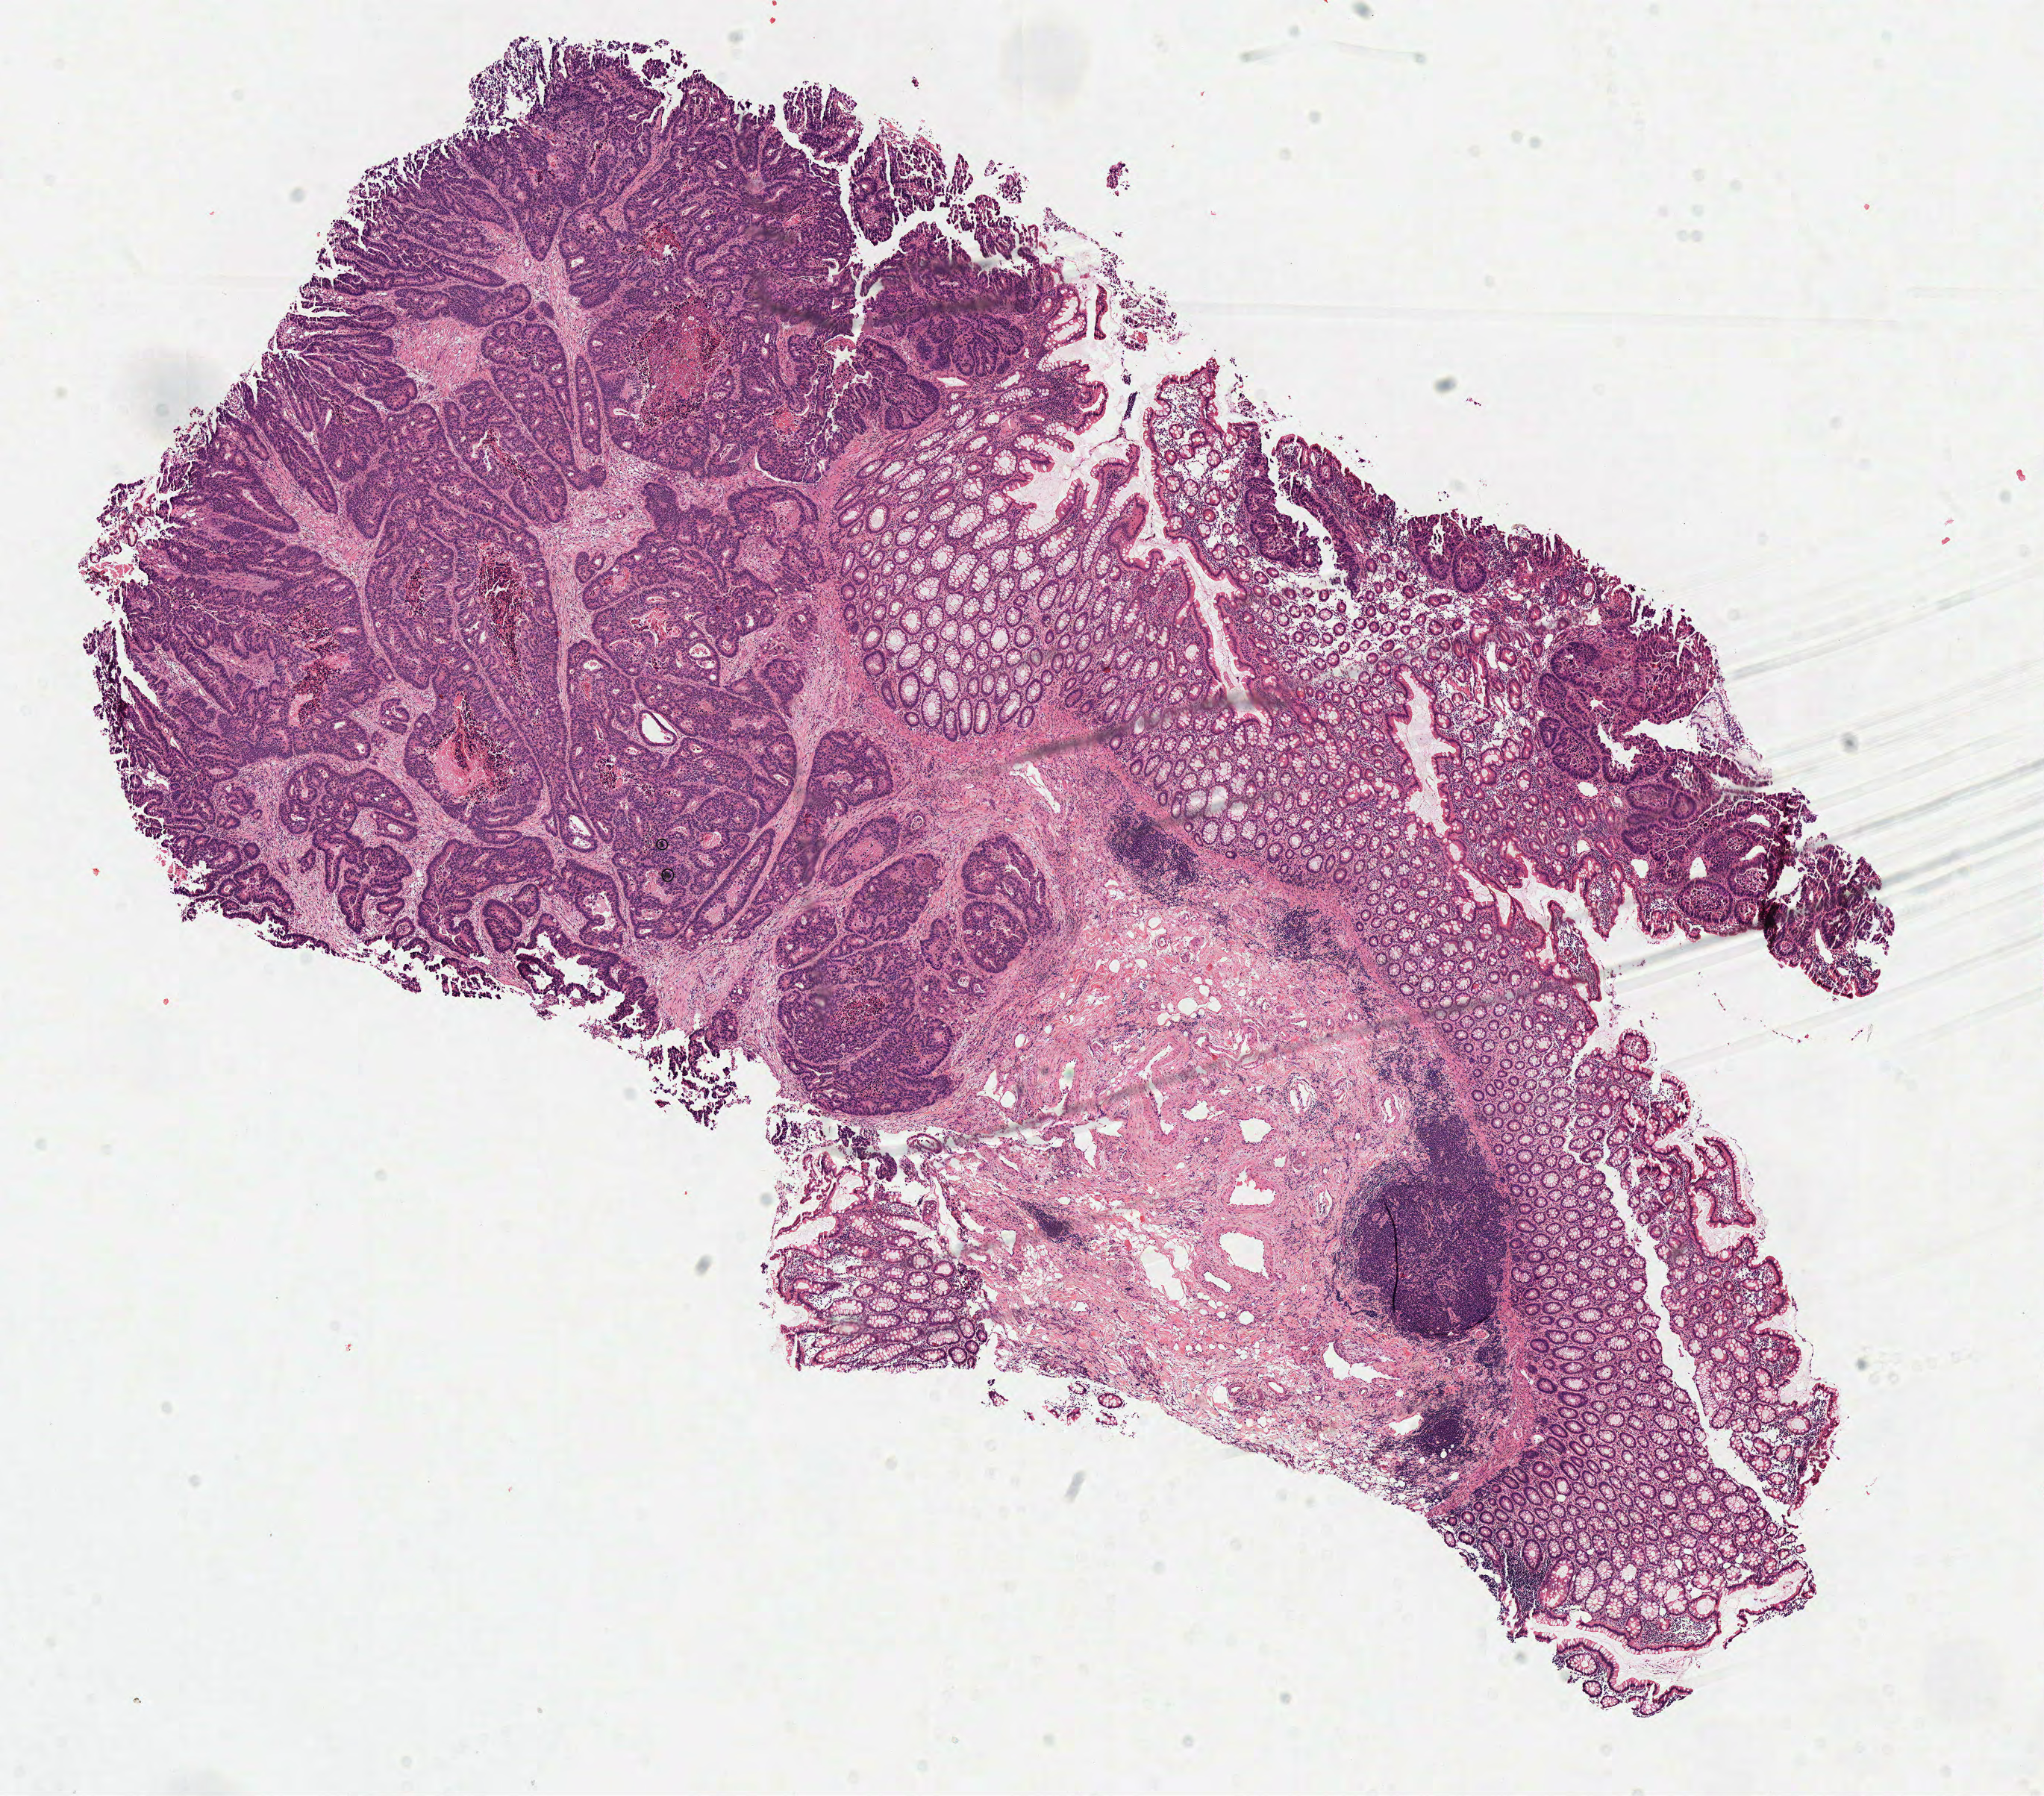
Digitized H&E-stained tissue section (whole slide), shown as a low-resolution overview of the whole scanned area (about 10.8 x 9.5 mm), frozen section from the top of the tissue portion, colon, primary tumour sample. Patient: female, age at initial diagnosis 55 years.
Diagnosis: Adenocarcinoma, NOS (cecum).